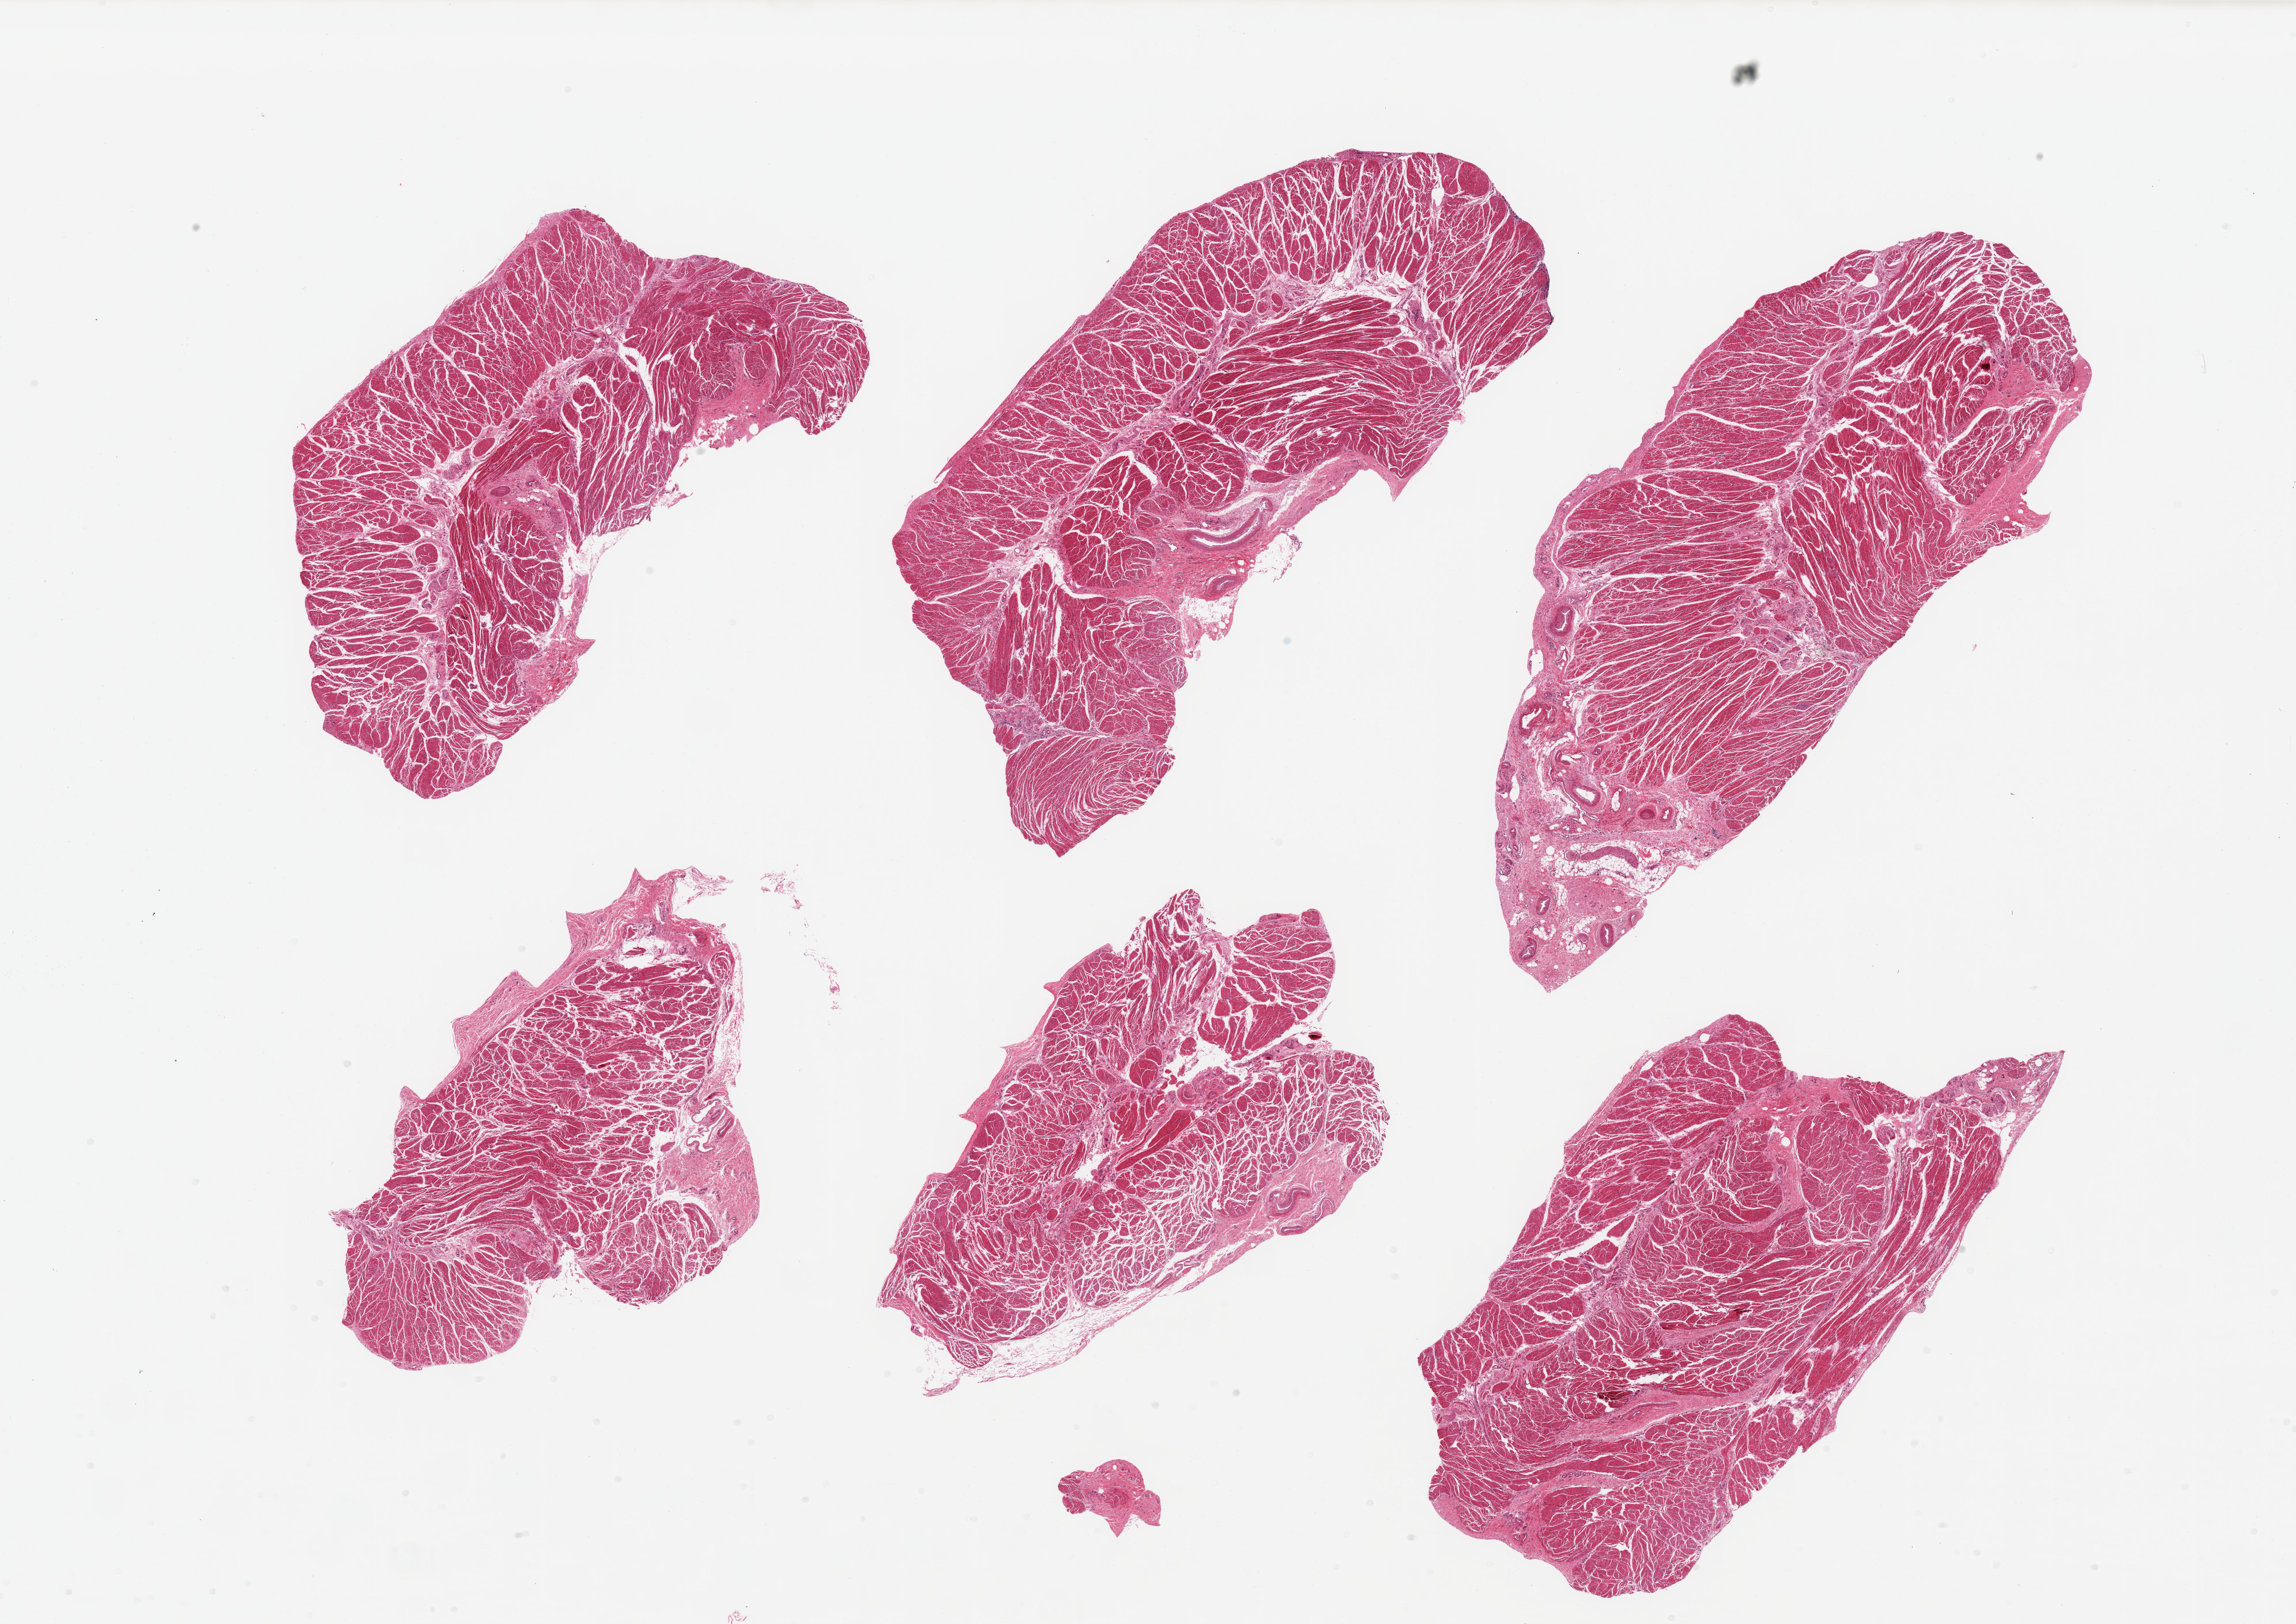
Digitized H&E-stained section, whole scanned area (about 31.5 x 22.3 mm, slide scanned at 20x) shown as a low-resolution overview. PAXgene-fixed, paraffin-embedded tissue. Sampled site (target tissue): gastroesophageal junction. Tissue donor sample. Donor: female.
Review note (as recorded): 6 pieces; well trimmed target muscularis.